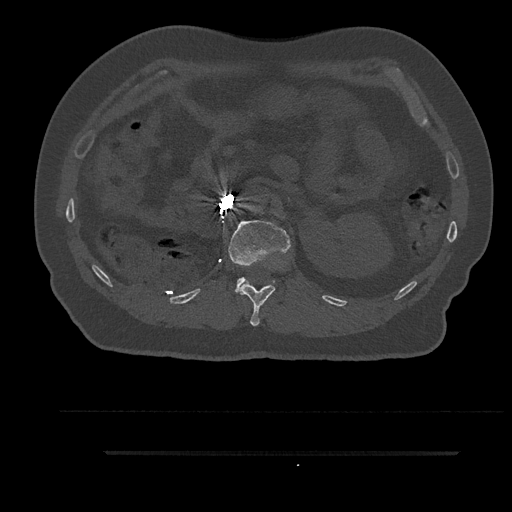
CT including the spine, one axial slice; slice 208 of 797 in the series (ordered by position); reconstruction kernel Br40s/3; bone window (W 1800 / L 400 HU); 0.5 mm slice thickness; 512 × 512 image matrix, field of view 432 × 432 mm. Male patient, age 63 years. Case-level facts recorded for this patient, not image findings: primary cancer: renal.
Structures marked on this image (semi-automatic segmentation, software-assisted and operator-edited):
- L1 vertebra: box from (x=228, y=220) to (x=291, y=293) px
- T12 vertebra: (x=239, y=281)–(x=275, y=326)